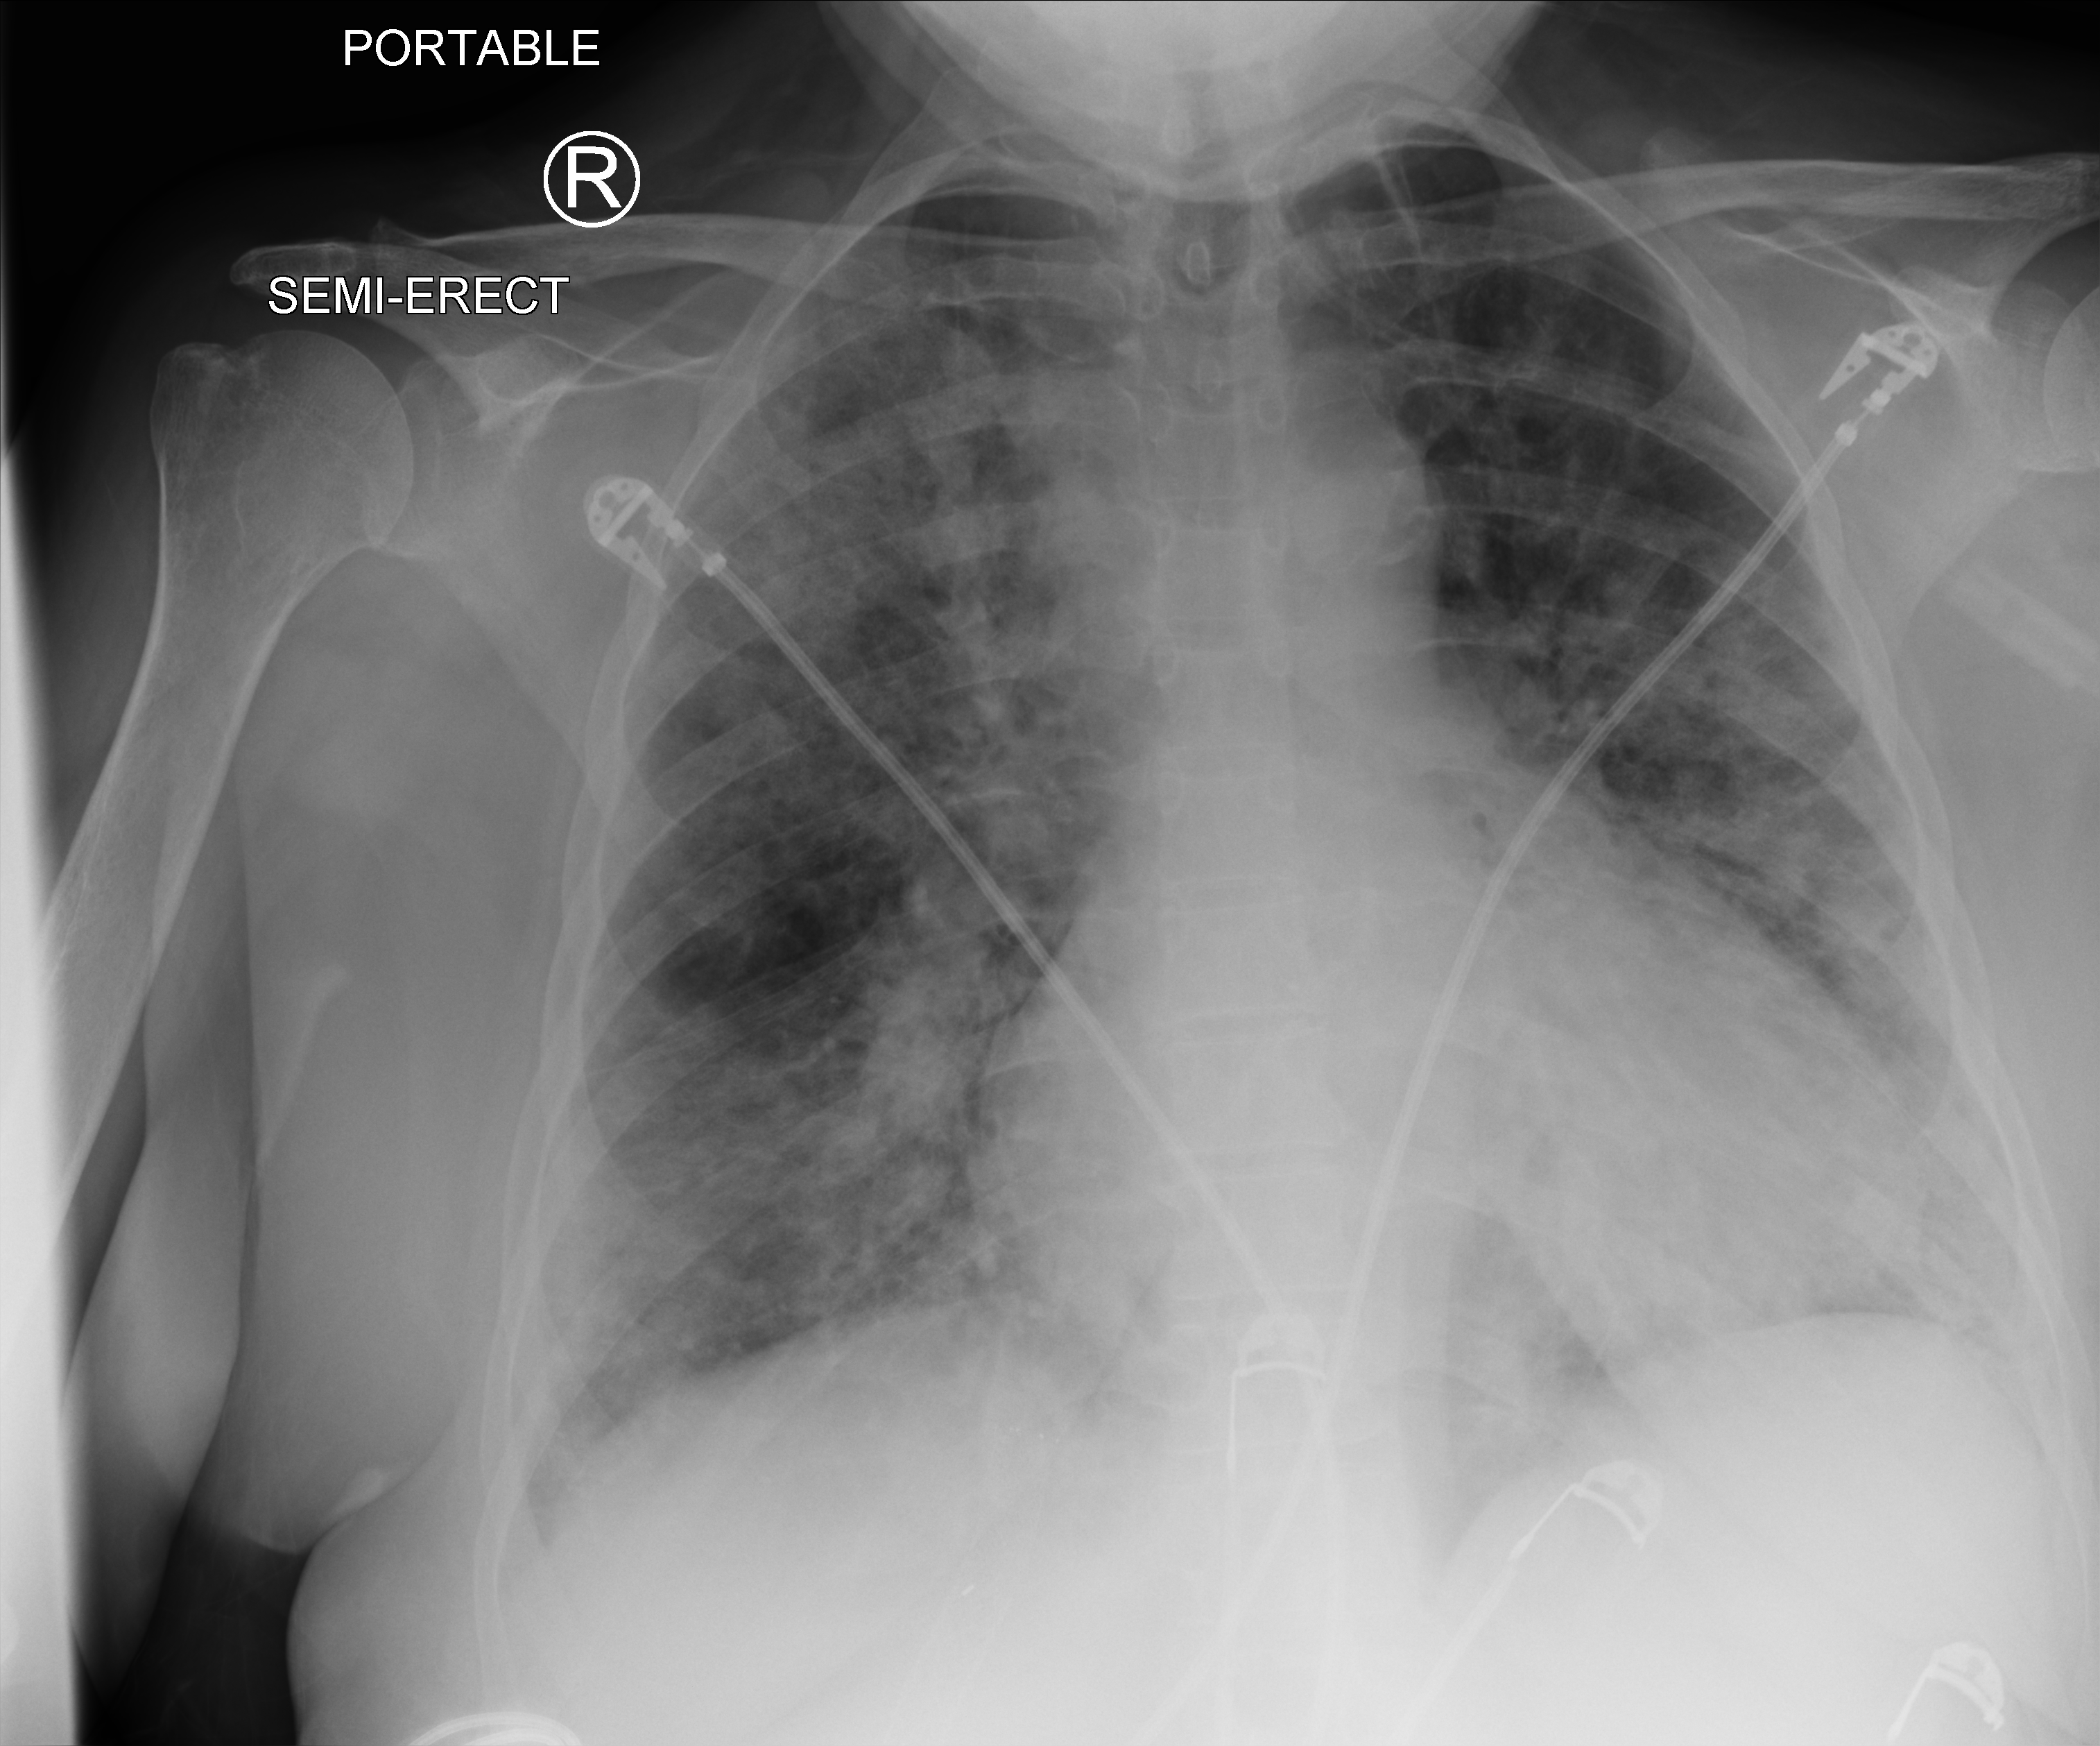
Bedside chest radiograph (computed radiography); anteroposterior (AP) projection. Female patient hospitalised with COVID-19, age 60–74 years.
From the hospital-stay record, not from the radiograph (when in the stay this image was taken is not recorded): mechanically ventilated during this hospital stay: no; admitted to intensive care during this hospital stay: yes.